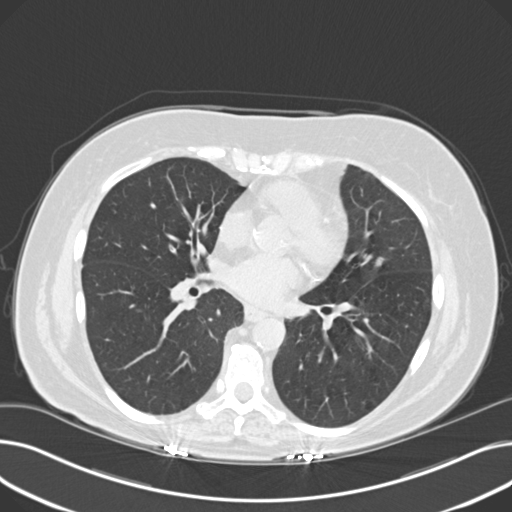
Low-dose screening chest CT, one axial slice. Position 93 of 203 along the scan axis. Reconstruction kernel B30f. 120 kVp. Lung window (W 1500 / L -600 HU). 2 mm slice thickness. 512 × 512 image matrix.
Structures marked on this image (outlined manually by an expert reader):
- lesion 1 (tumor, upper lobe of left lung): bounding box (x1, y1, x2, y2) in pixels: (374, 257, 385, 268)